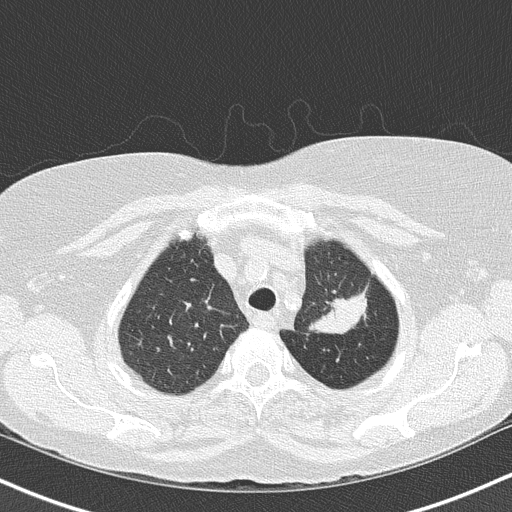
Chest CT (low-dose screening protocol), one axial image. Third annual screen. Lung window (W 1500 / L -600 HU). 2 mm slice thickness. Female participant, aged 68 years at enrolment.
Expert-annotated lung lesion, bounding box <290,234,380,340> (left, top, right, bottom; pixels). The exam's reader record, not a measurement of the box and not confirmed to be the same lesion: non-calcified nodule or mass ≥4 mm, left upper lobe, 5 × 5 mm, poorly defined margins, mixed attenuation, pre-existing on the prior screen: yes; interval growth: yes. Lung cancer was diagnosed 42 days after this screen: adenocarcinoma, NOS, left upper lobe, poorly differentiated (G3), stage IB (AJCC 6th edition), 50 mm at pathology.